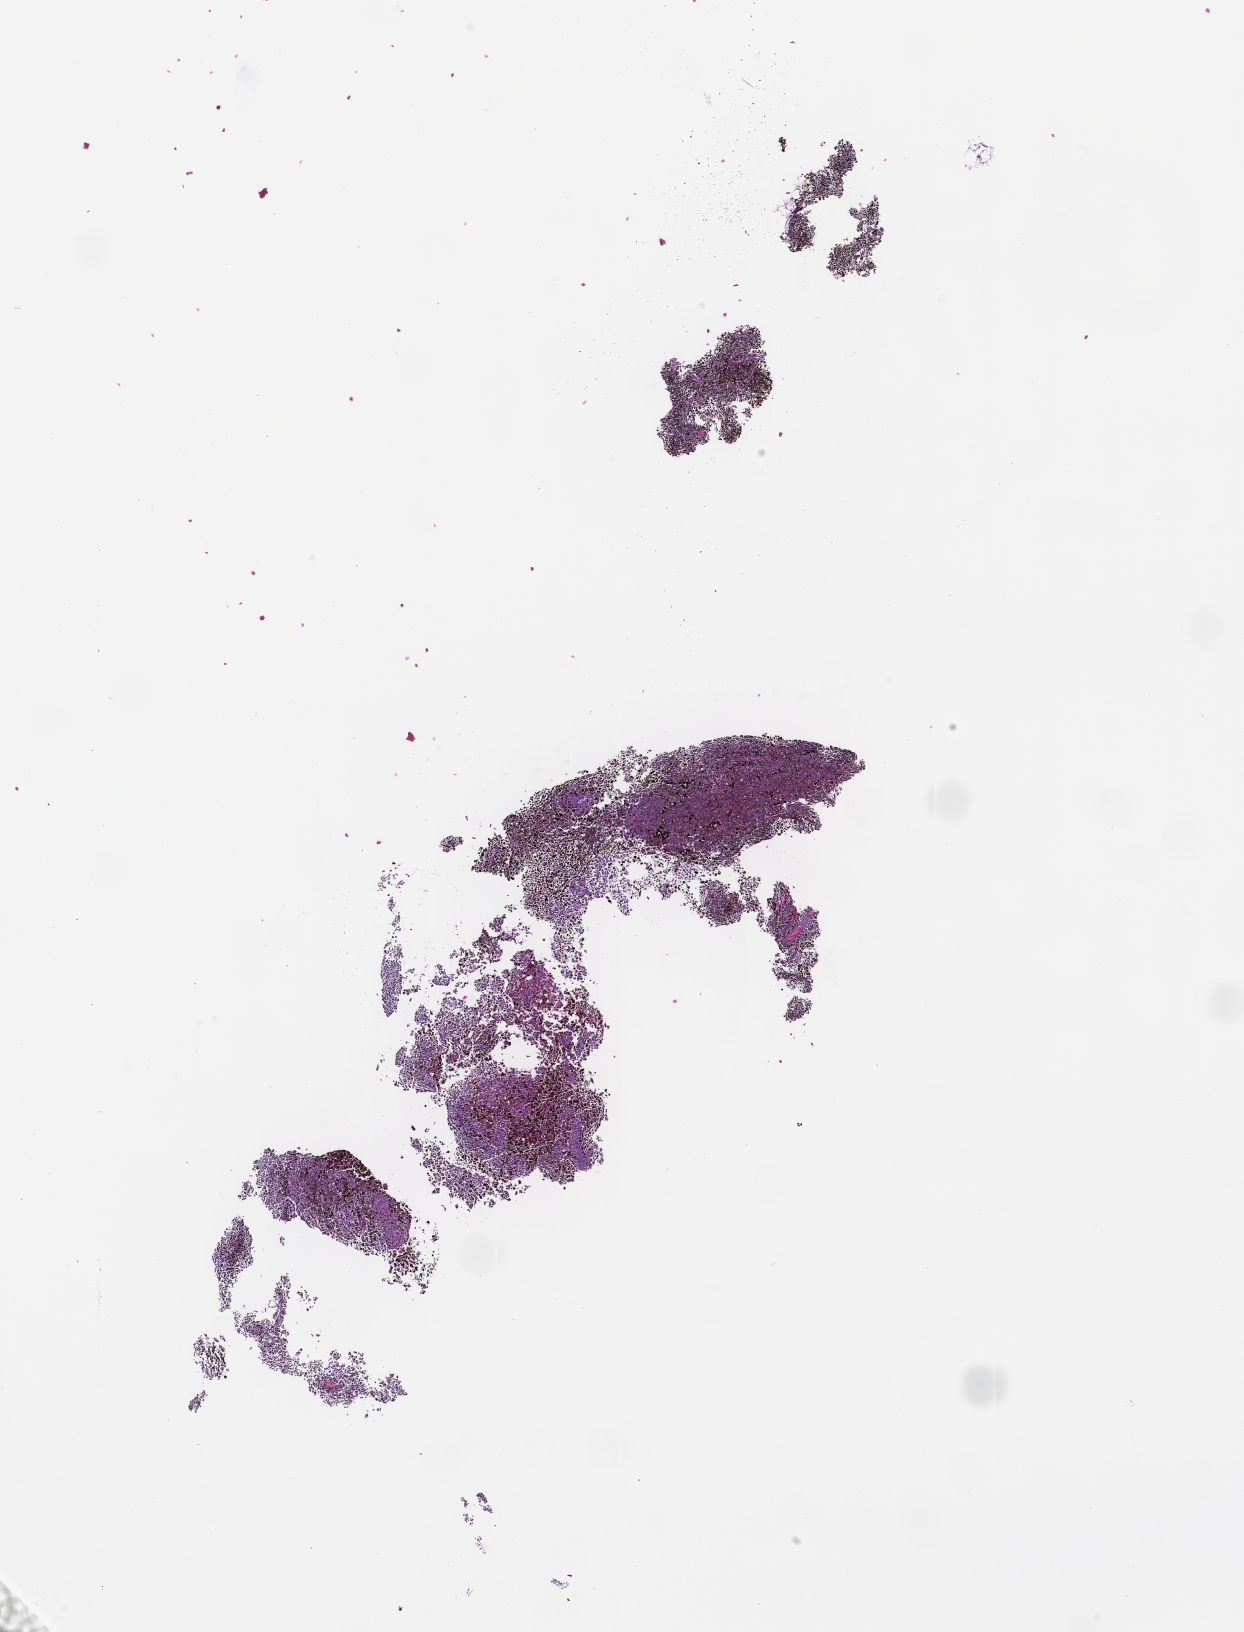
H&E whole-slide image, whole scanned area (about 10.1 x 13.2 mm) shown as a low-resolution overview, formalin-fixed paraffin-embedded section, collected at baseline (before treatment). Male patient.
This section: metastatic tumor tissue. Patient diagnosis (primary): Melanoma.